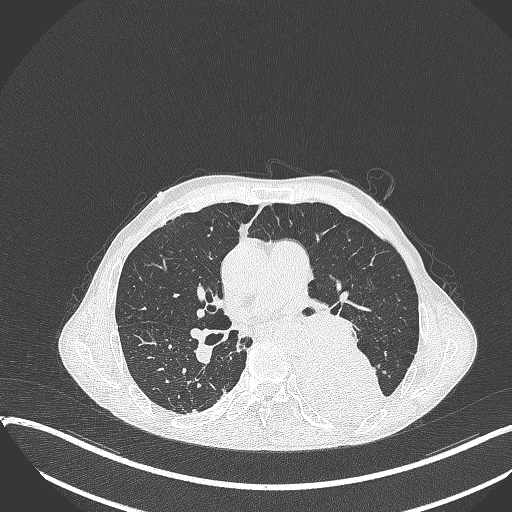
Chest CT, one axial slice; position 204 of 401 along the scan axis; reconstruction kernel B70f; lung window (W 1500 / L -600 HU); 1 mm slice thickness; 512 × 512 image matrix, field of view 400 × 400 mm. Male patient, age 57 years. Case-level facts recorded for this patient, not image findings: clinical TNM (as recorded): T4 N0 M0.
Outlined on this slice (rectangle marked by the reading radiologist):
- lung tumour (recorded histology: squamous cell carcinoma): bounding box <293,346,394,419> (left, top, right, bottom; pixels)